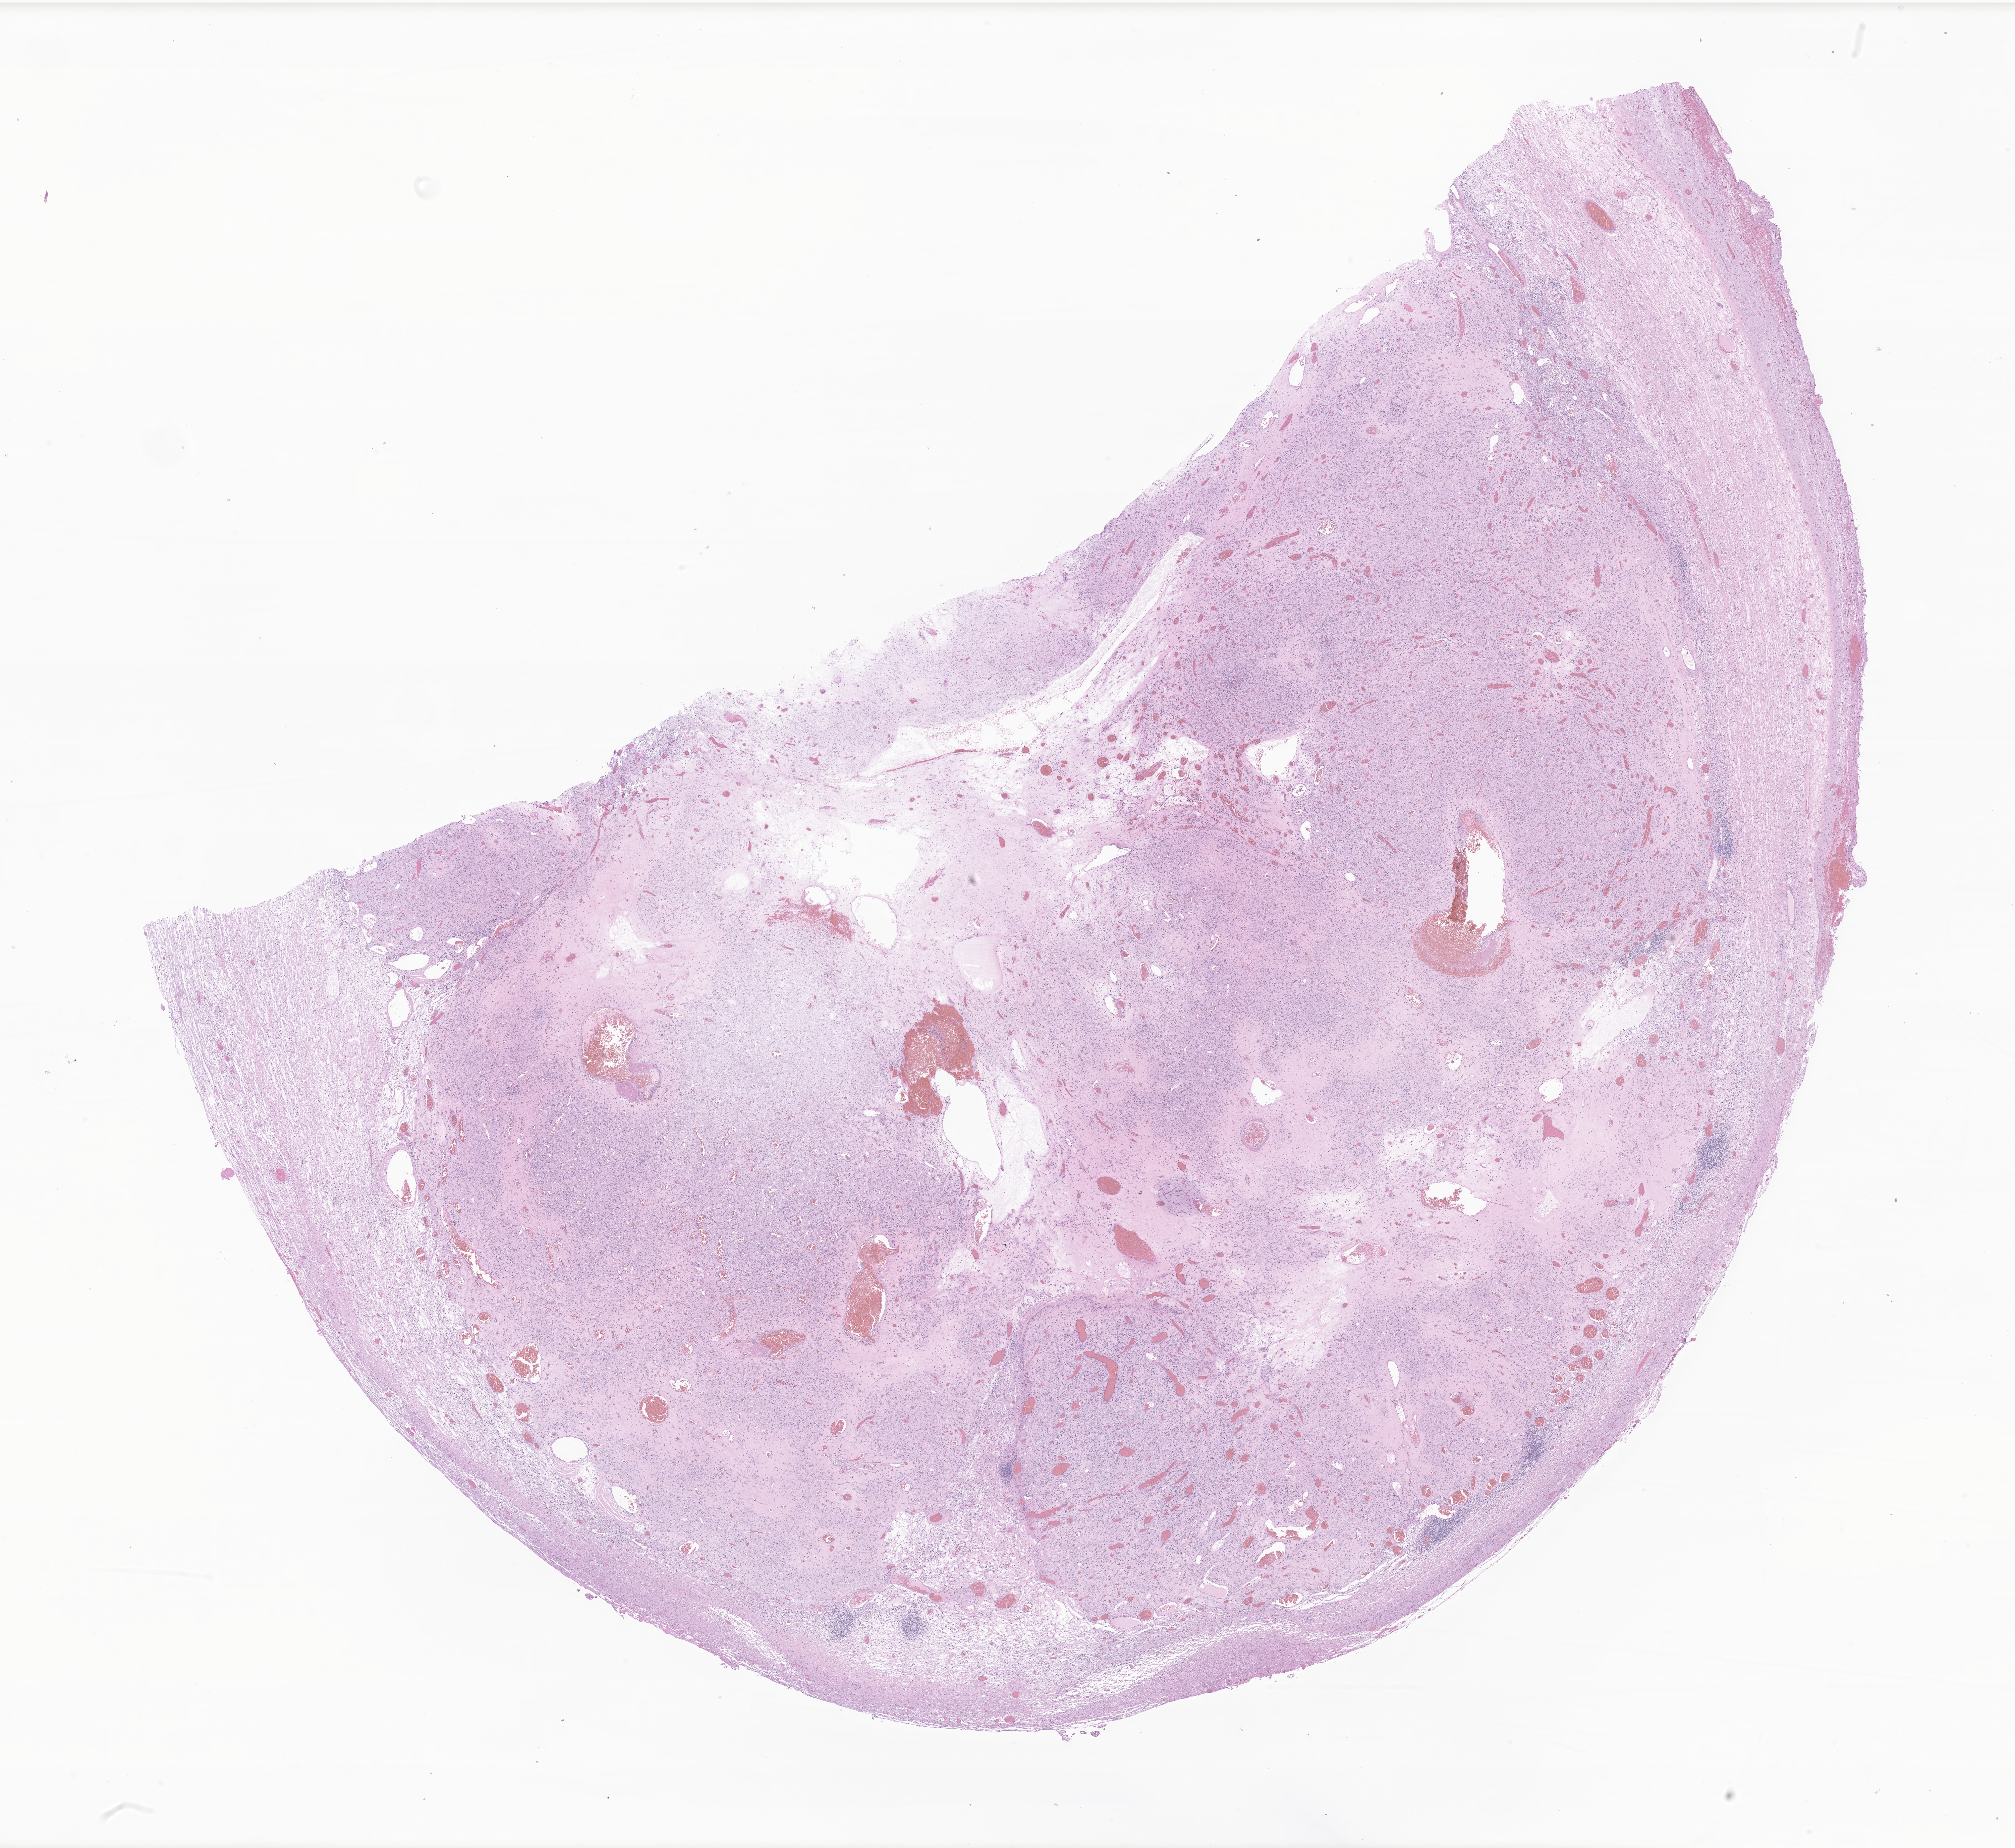
Haematoxylin and eosin whole-slide image of tumor tissue from the frontal lobe, low-resolution overview of the scanned area, about 25.3 x 23.2 mm; formalin-fixed, paraffin-embedded (FFPE) tissue. Patient female; age 120 months (10 years).
• diagnosis: Myofibroblastic tumor, NOS